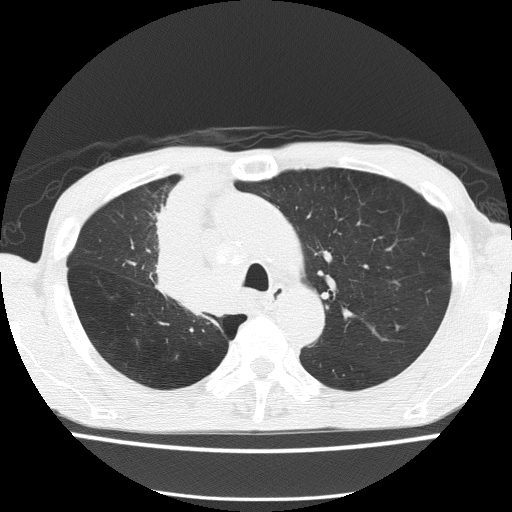
Low-dose screening chest CT, one axial slice; slice 106 of 150 in the series (ordered by position); reconstruction kernel FC51; lung window (W 1500 / L -600 HU); 512 × 512 image matrix, field of view 336 × 336 mm.
Outlined on this slice (manually delineated by an expert):
- lesion 1 (tumor, hilum of right lung): bounding box (x1, y1, x2, y2) in pixels: (159, 180, 210, 313)